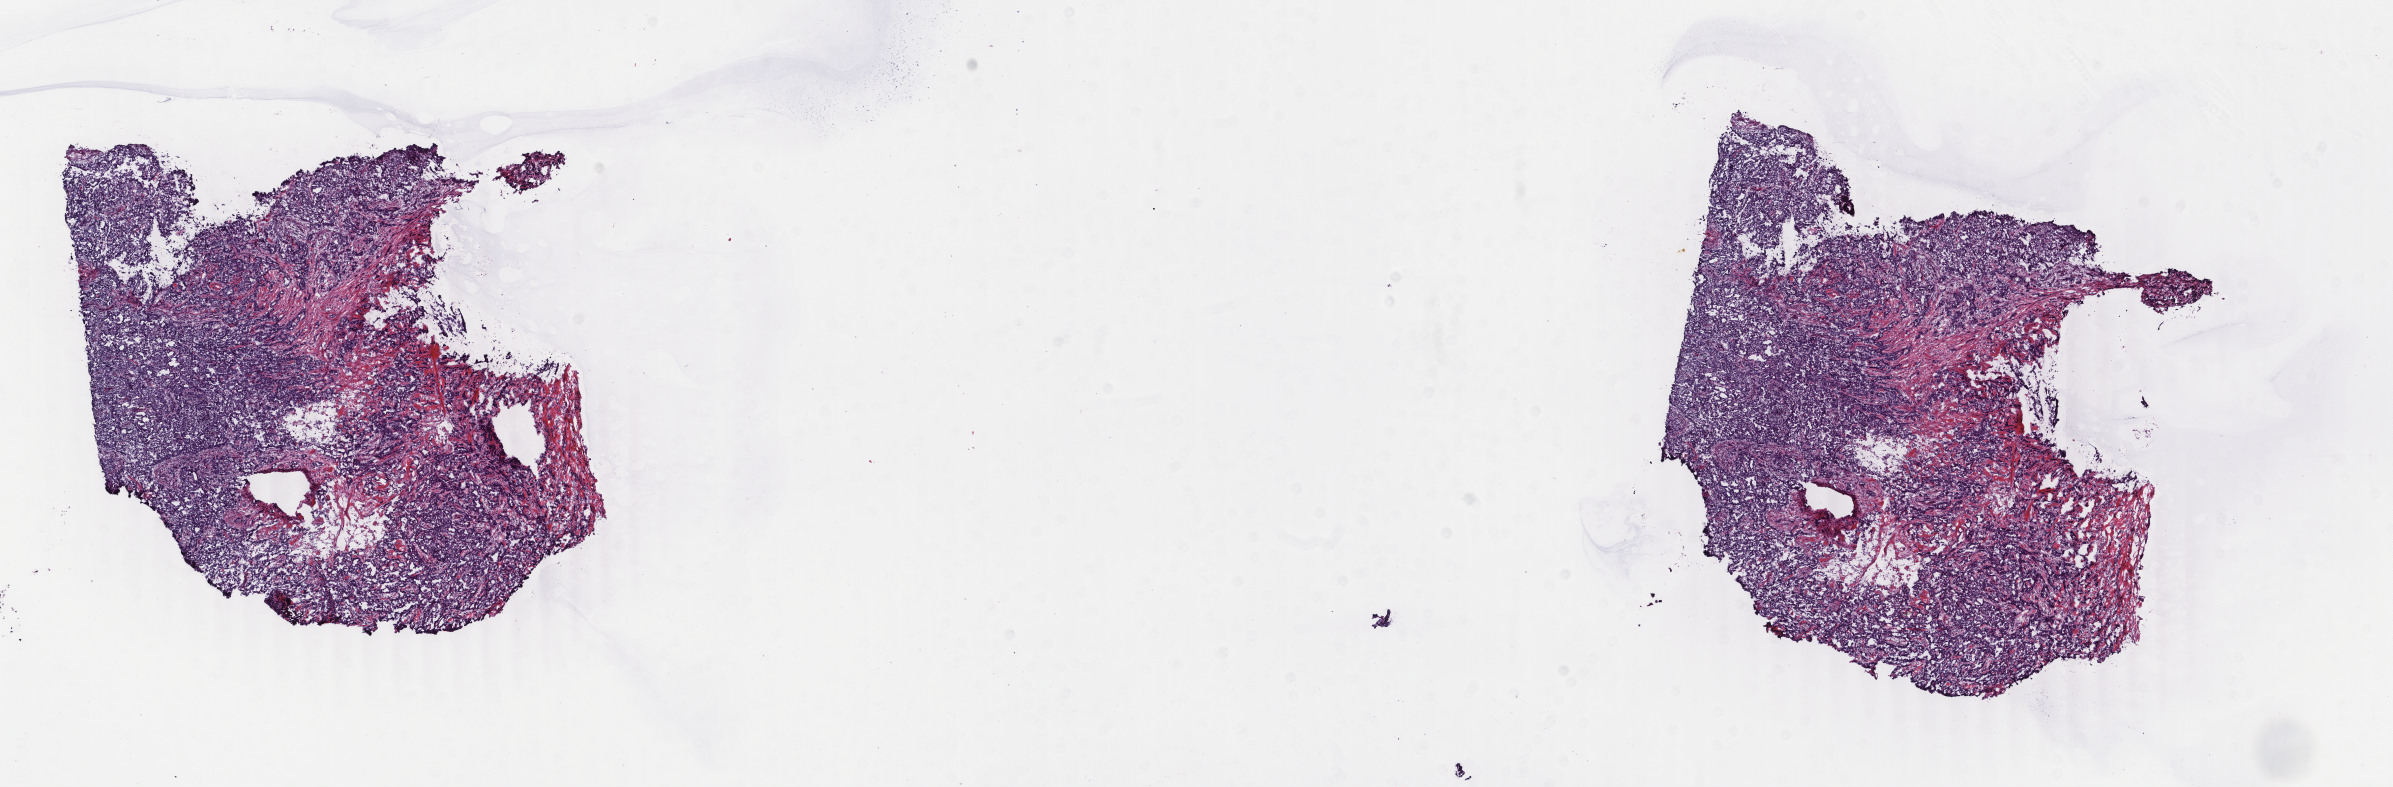
Hematoxylin and eosin (H&E) stained whole-slide image — whole scanned area (about 19.0 x 6.3 mm, from a 40x scan) shown as a low-resolution overview, frozen section from the bottom of the tissue portion, sample: primary tumour, breast. Female patient; age at initial diagnosis 45 years. Slide review estimates, as recorded: tumour cells 90%, tumour nuclei 70%, normal cells 0%, stromal cells 10%, necrosis 0%. Inflammatory infiltration, as recorded: lymphocyte infiltration 0%, monocyte infiltration 0%, neutrophil infiltration 0%.
Histologic diagnosis: Infiltrating duct carcinoma, NOS. Laterality: right. Lymph nodes positive (case pathology): 0 of 1 examined.